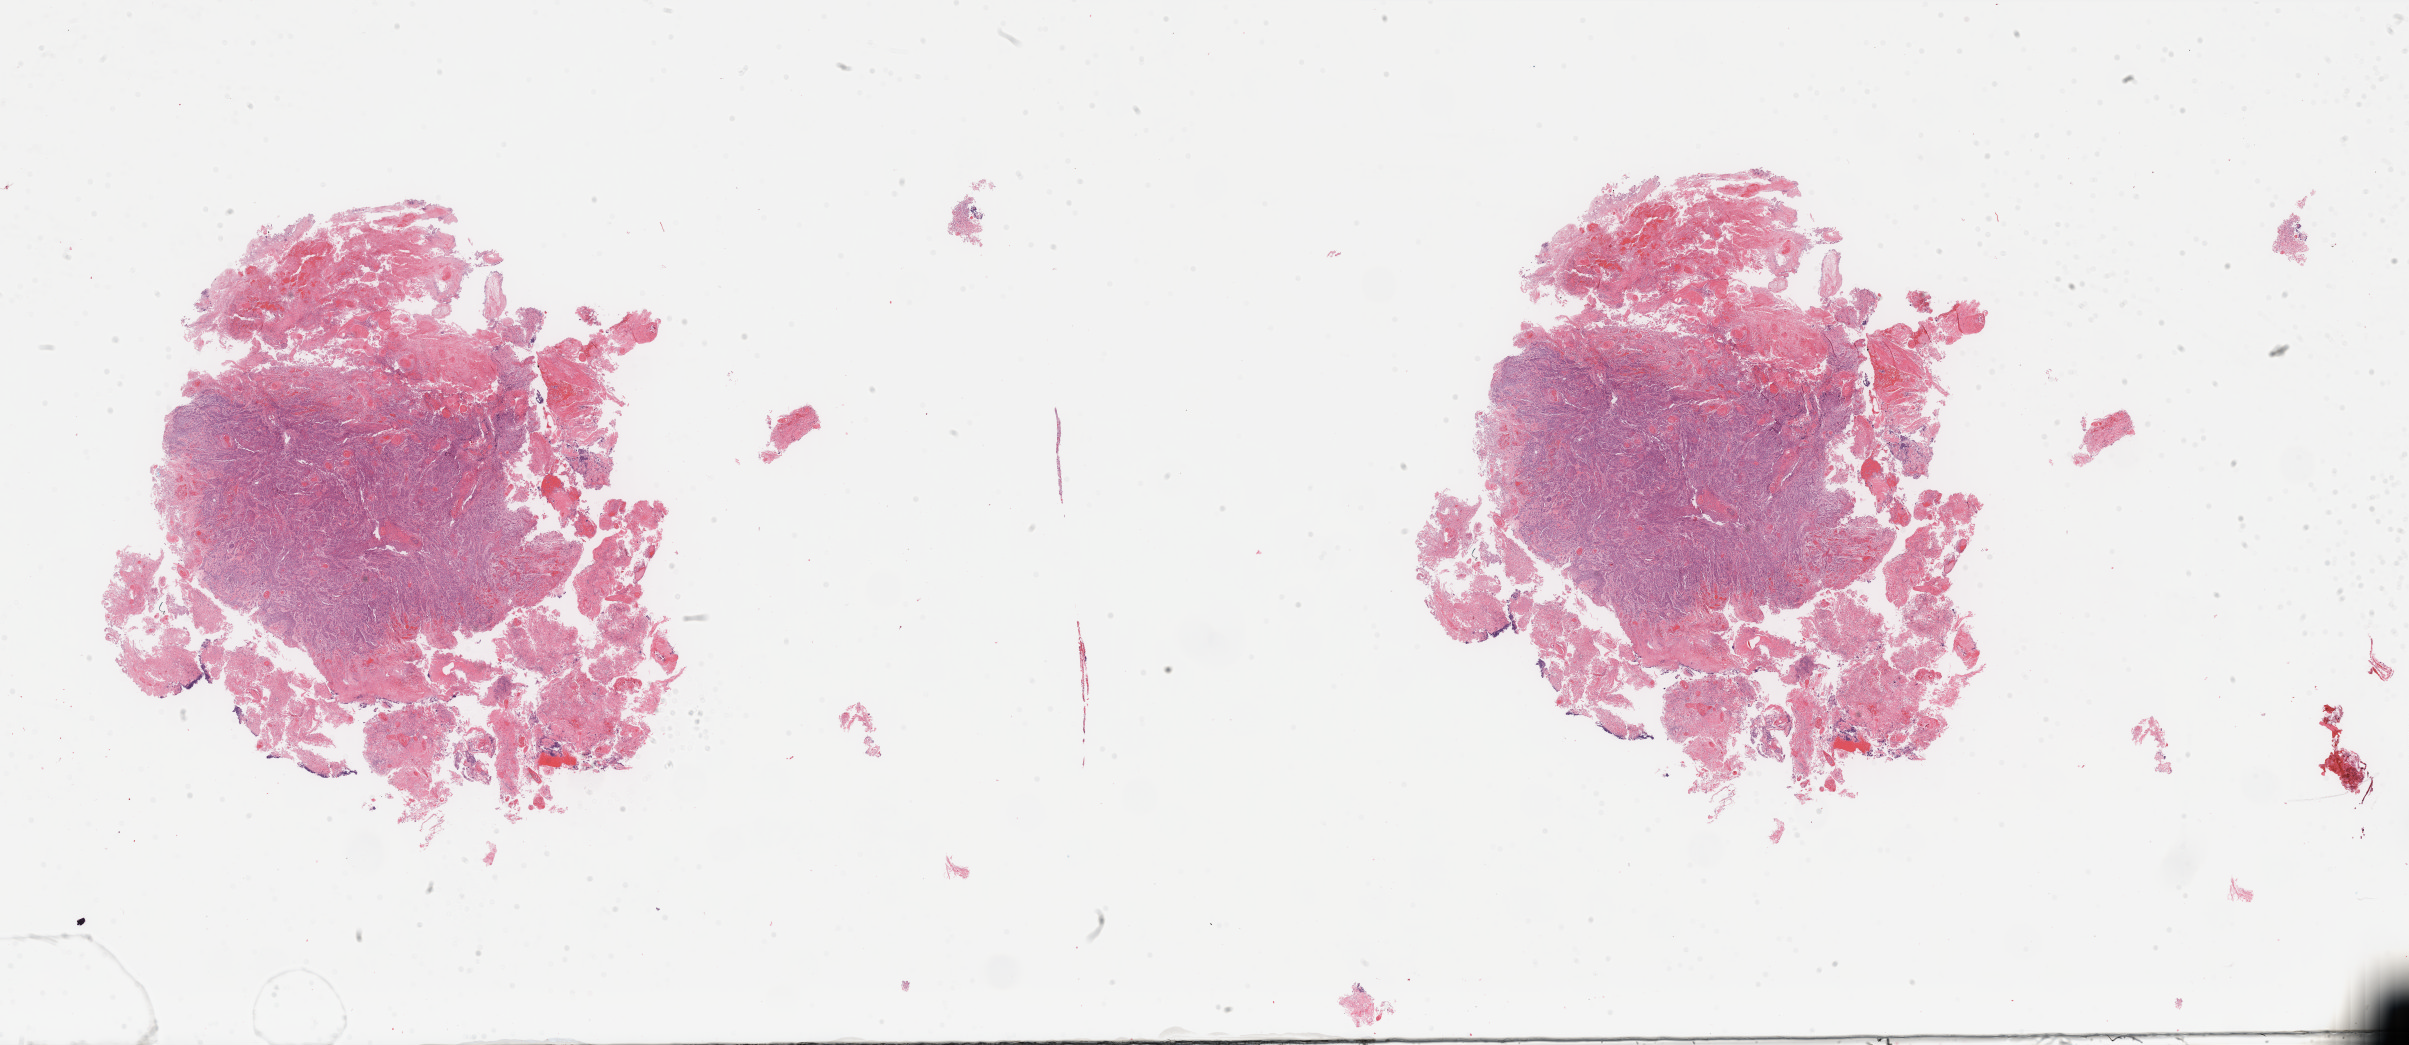
Digitized H&E-stained tissue section (whole slide), low-resolution overview of the scanned area, about 38.1 x 16.5 mm (slide scanned at 40x), FFPE section, primary tumour sample from the head and neck. Patient: male, age at initial diagnosis 49 years. Histologic grade: G2 (moderately differentiated).
Diagnosis: Squamous cell carcinoma, NOS (tongue, NOS).